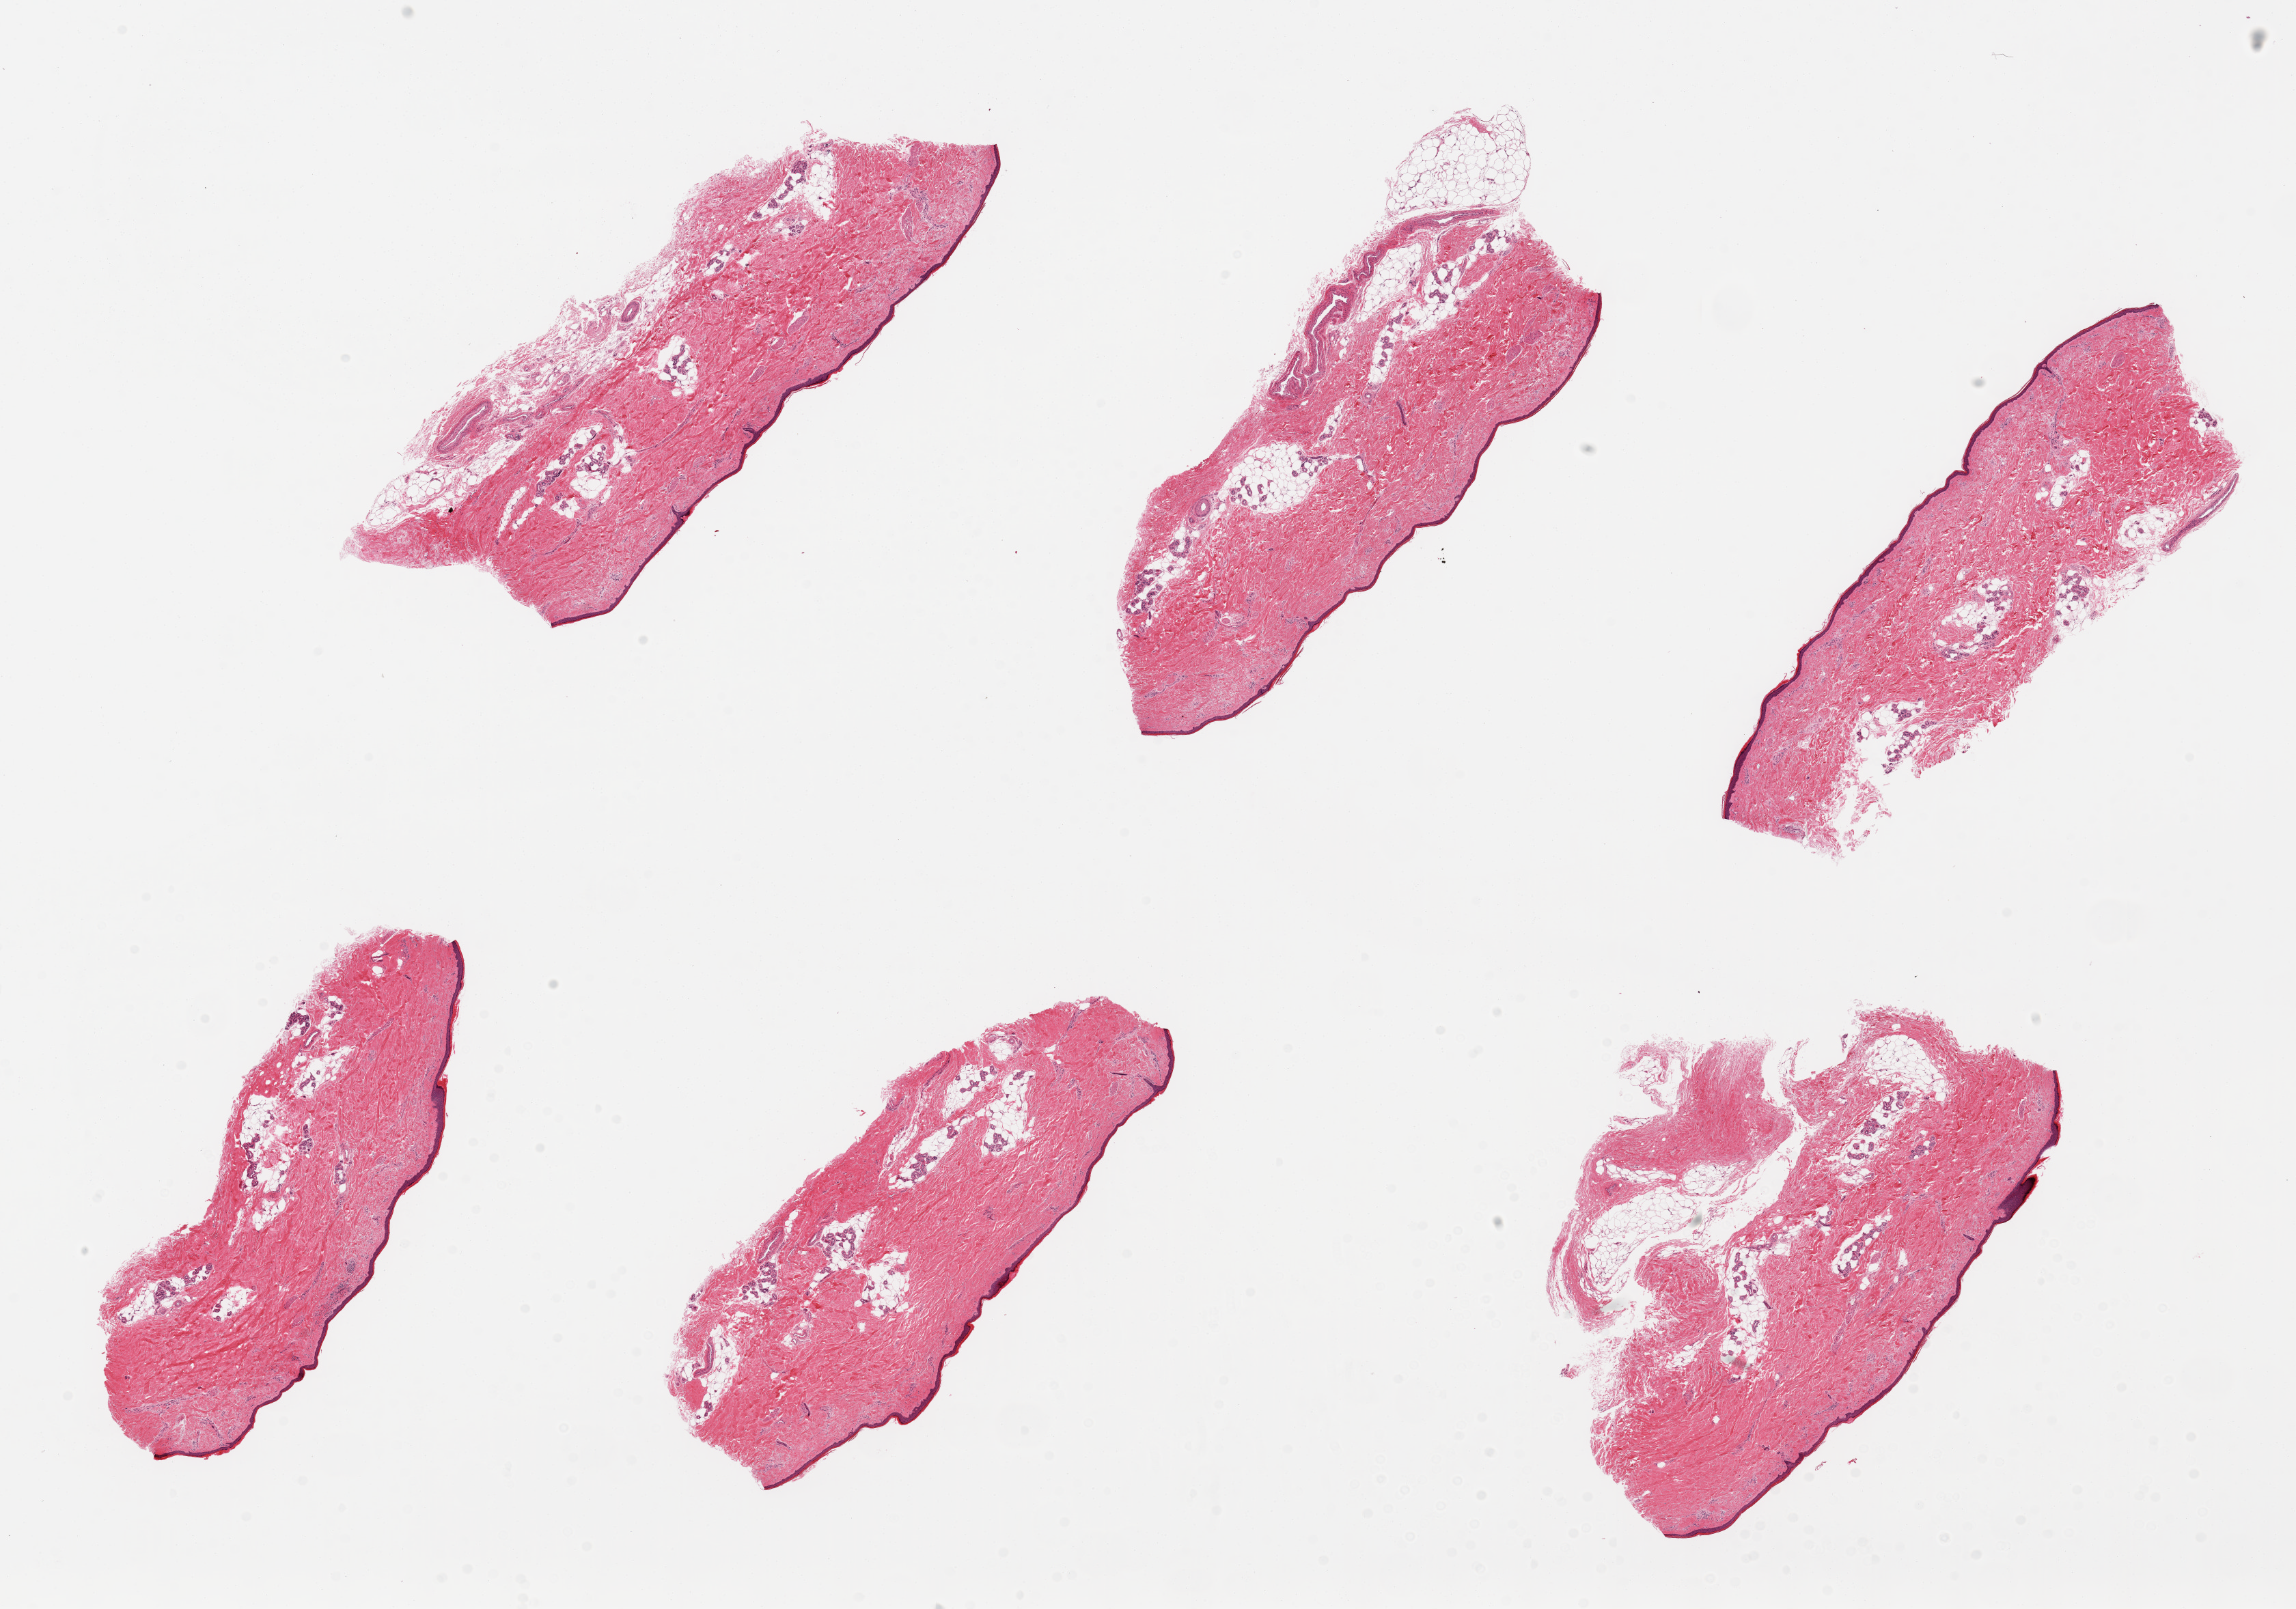
Whole-slide image, H&E stain — a low-resolution overview of the entire scanned area, about 26.6 x 18.6 mm (slide scanned at 20x). PAXgene-fixed, paraffin-embedded tissue. Target tissue: skin of lower leg. Tissue donor sample. Donor: female.
Pathologist's review note for this sample: 6 pieces. up to 8x3mm; subcutaneous adipose in 2/6.